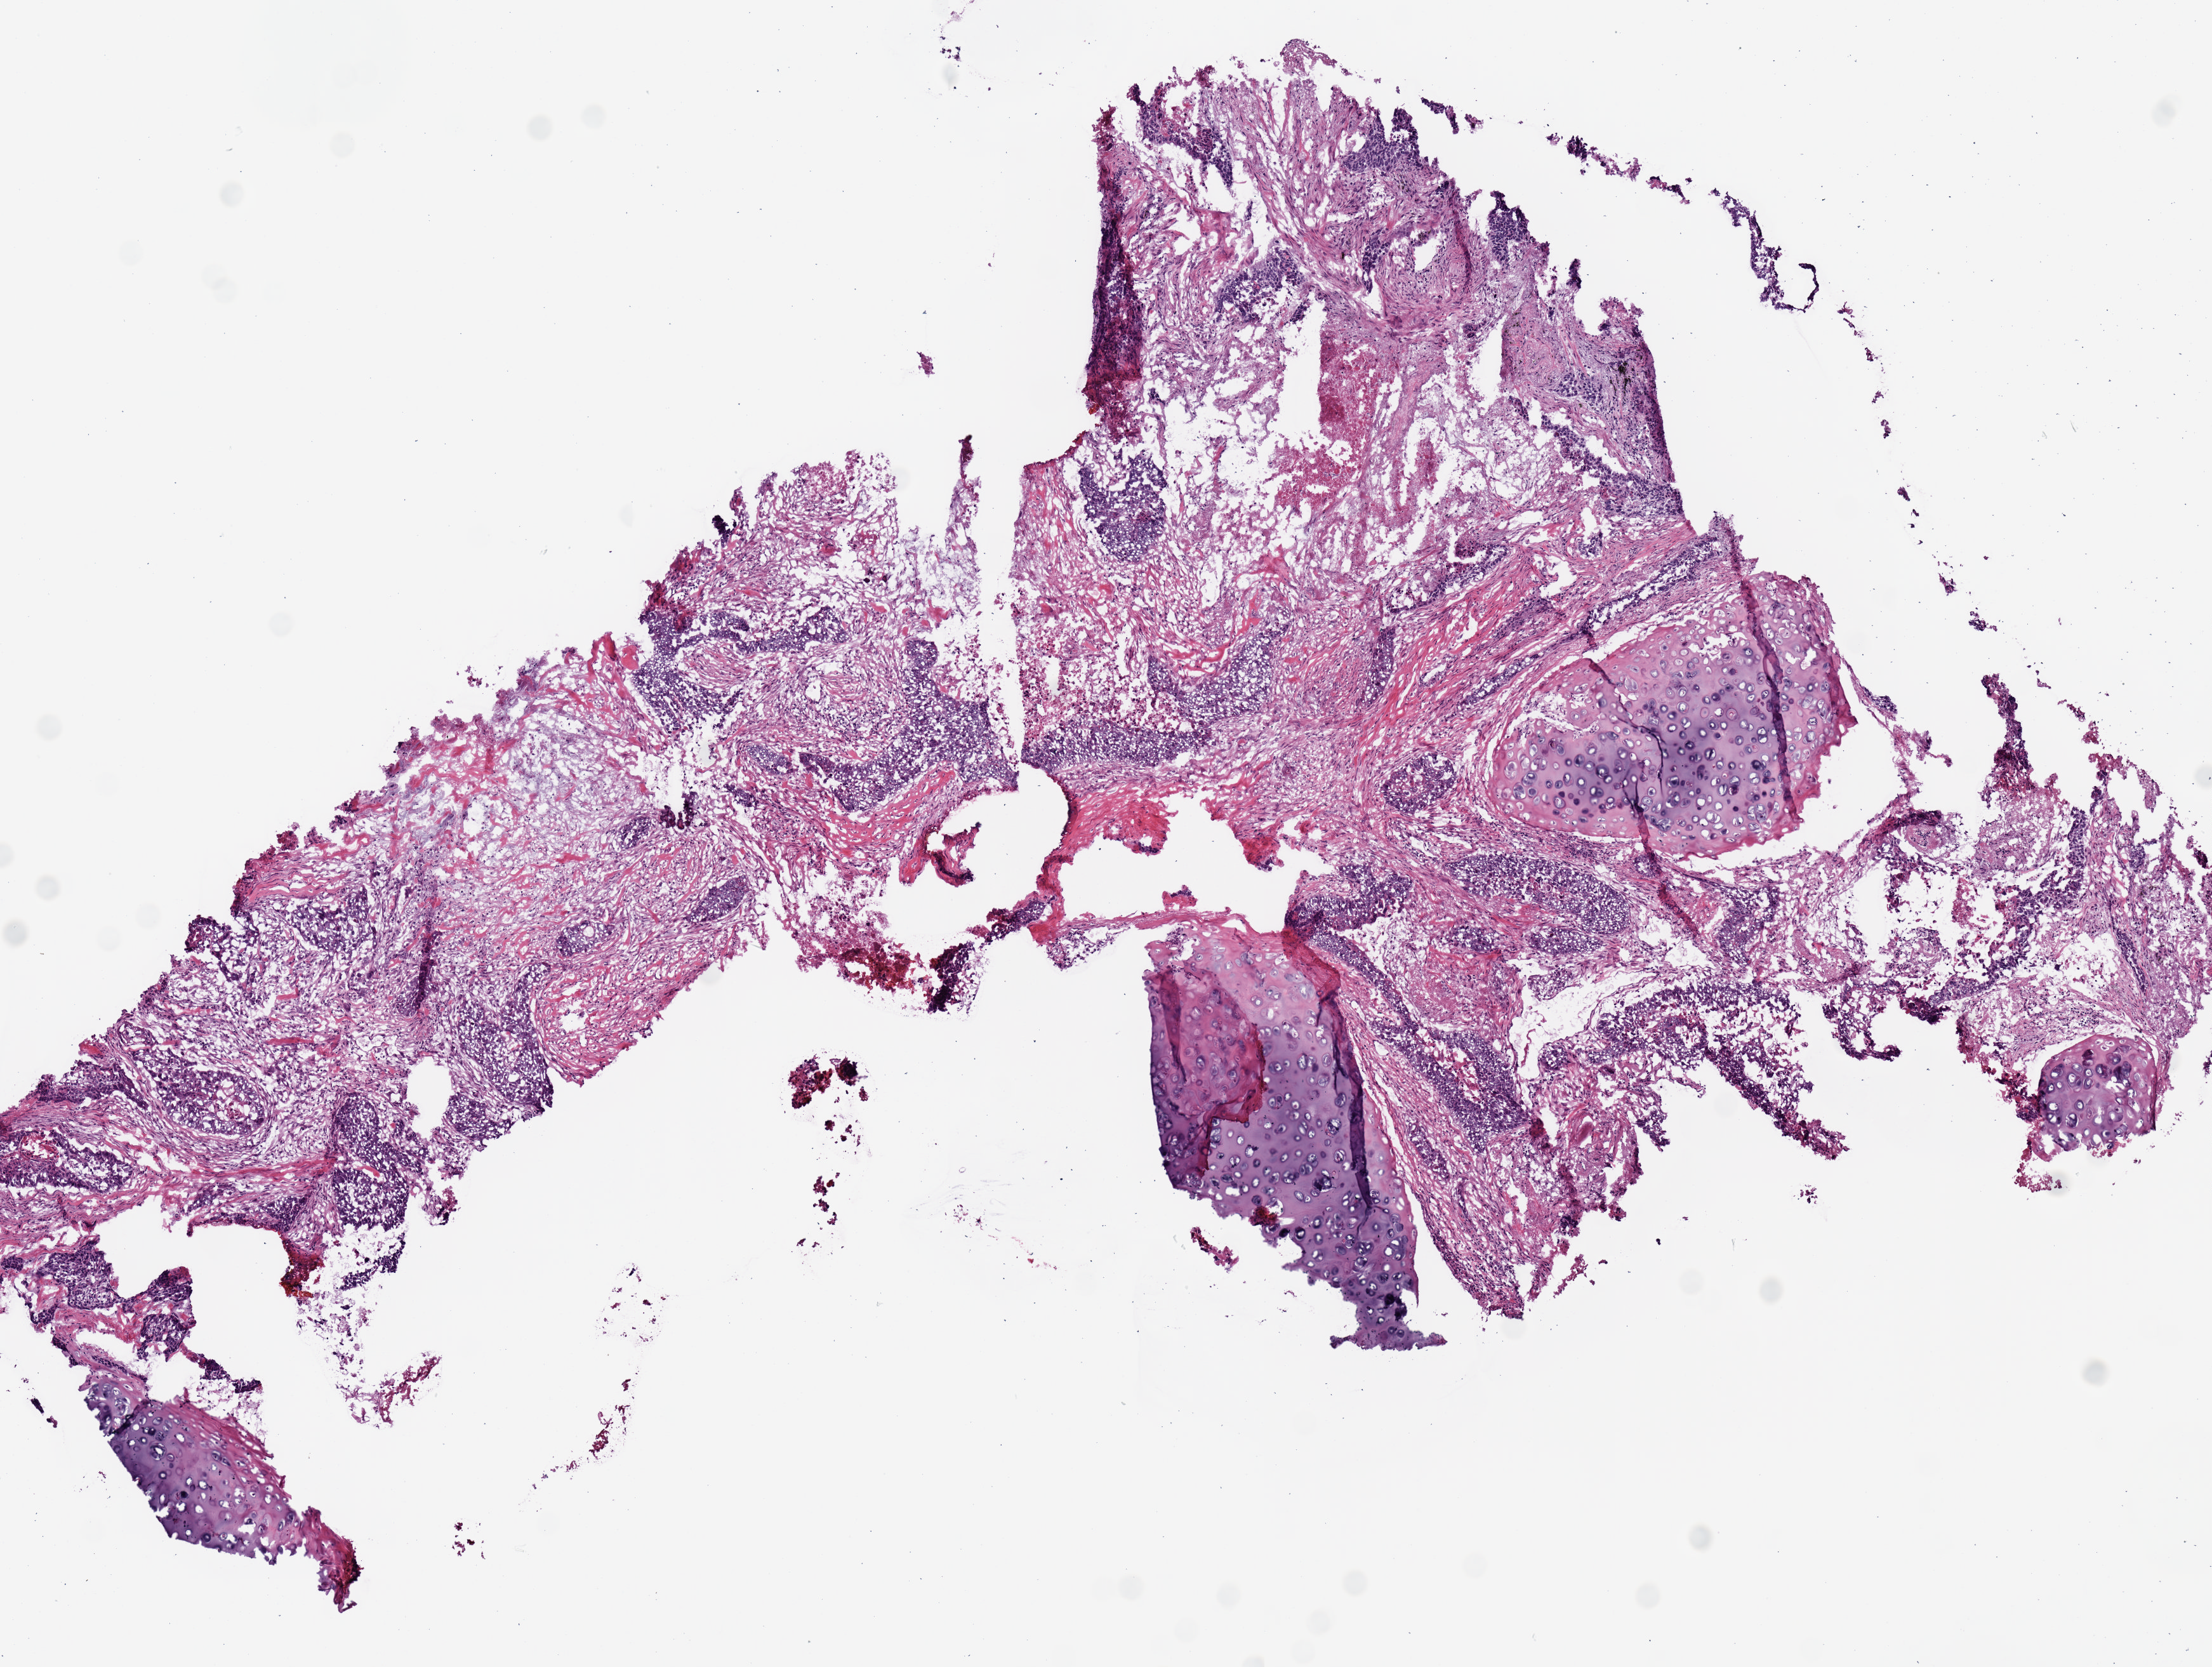
Hematoxylin and eosin (H&E) stained whole-slide image — shown as a low-resolution overview of the whole scanned area (about 6.9 x 5.2 mm), frozen section from the top of the tissue portion, sample: primary tumour, lung. Patient: male, age at initial diagnosis 60 years. Pathologist review of this section (percent, as recorded): tumour nuclei 70%, necrosis 10%.
Histologic diagnosis: Squamous cell carcinoma, NOS. AJCC pathologic stage: IIIA (6th edition).